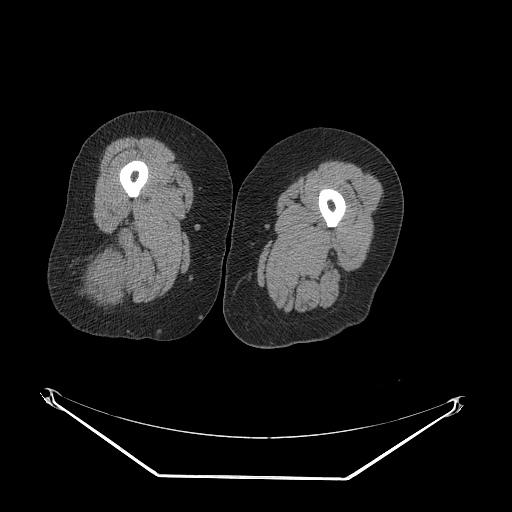
CT of an extremity soft-tissue mass (from a PET/CT study), one axial slice; position 27 of 257 along the scan axis; reconstruction kernel STANDARD; 140 kVp; soft-tissue window (W 400 / L 40 HU); 3.75 mm slice thickness; 512 × 512 image matrix, field of view 500 × 500 mm. Female patient. Case-level facts recorded for this patient, not image findings: histological type: synovial sarcoma; grade: intermediate; site of the primary tumour: right buttock.
Structures marked on this image (expert contour drawn on MRI and transferred to this co-registered scan by the dataset authors):
- gross tumour volume including surrounding oedema: bounding box <91,242,126,300> (left, top, right, bottom; pixels)
- gross tumour volume (mass): <91,256,122,300>